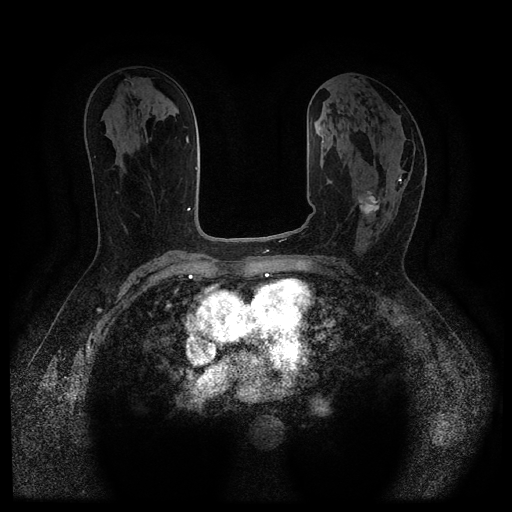
Breast MRI (dynamic contrast-enhanced, multi-phase), one axial slice; slice 56 of 116 in the series (ordered by position); dynamic contrast-enhanced series, time point 2 of 5 at this slice position (early post-contrast); 1.5 T; TE 2.6 ms, TR 5.4 ms; 2 mm slice thickness; 512 × 512 image matrix, field of view 340 × 340 mm. Patient: female, 64 years.
Outlined on this slice (semi-automatic segmentation, software-assisted and operator-edited):
- breast lesion (labelled 'tumour' in the annotation; benign lesions carry a separate 'benign' label): bounding box (x1, y1, x2, y2) in pixels: (357, 191, 380, 216)